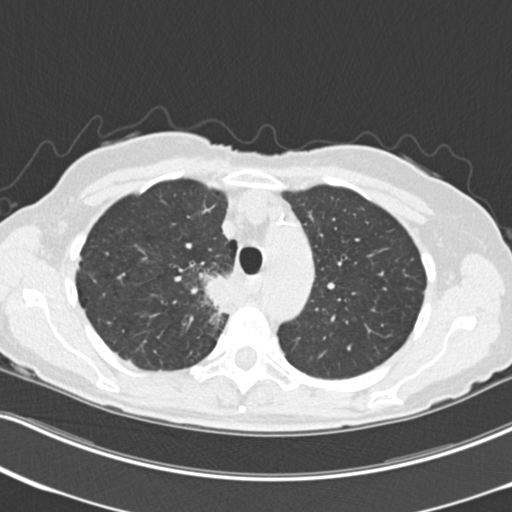
Low-dose screening chest CT, one axial slice; slice 171 of 226 in the series (ordered by position); reconstruction kernel B30f; lung window (W 1500 / L -600 HU); 2 mm slice thickness; 512 × 512 image matrix.
Outlined on this slice (expert manual segmentation):
- lesion 1 (tumor, mediastinum): bounding box (x1, y1, x2, y2) in pixels: (205, 275, 233, 315)